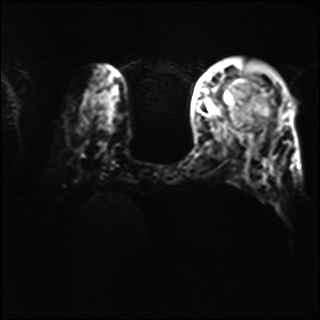
Breast MRI, one axial slice. Slice 16 of 40 in the series (ordered by position). Diffusion-weighted series; image 2 of 4 stored at this slice position (different b-values; order by instance number). 1.5 T. 4 mm slice thickness. 320 × 320 image matrix, field of view 320 × 320 mm. Female patient.
Structures marked on this image (manually delineated by an expert):
- tumour on diffusion-weighted imaging: box from (x=220, y=80) to (x=273, y=114) px